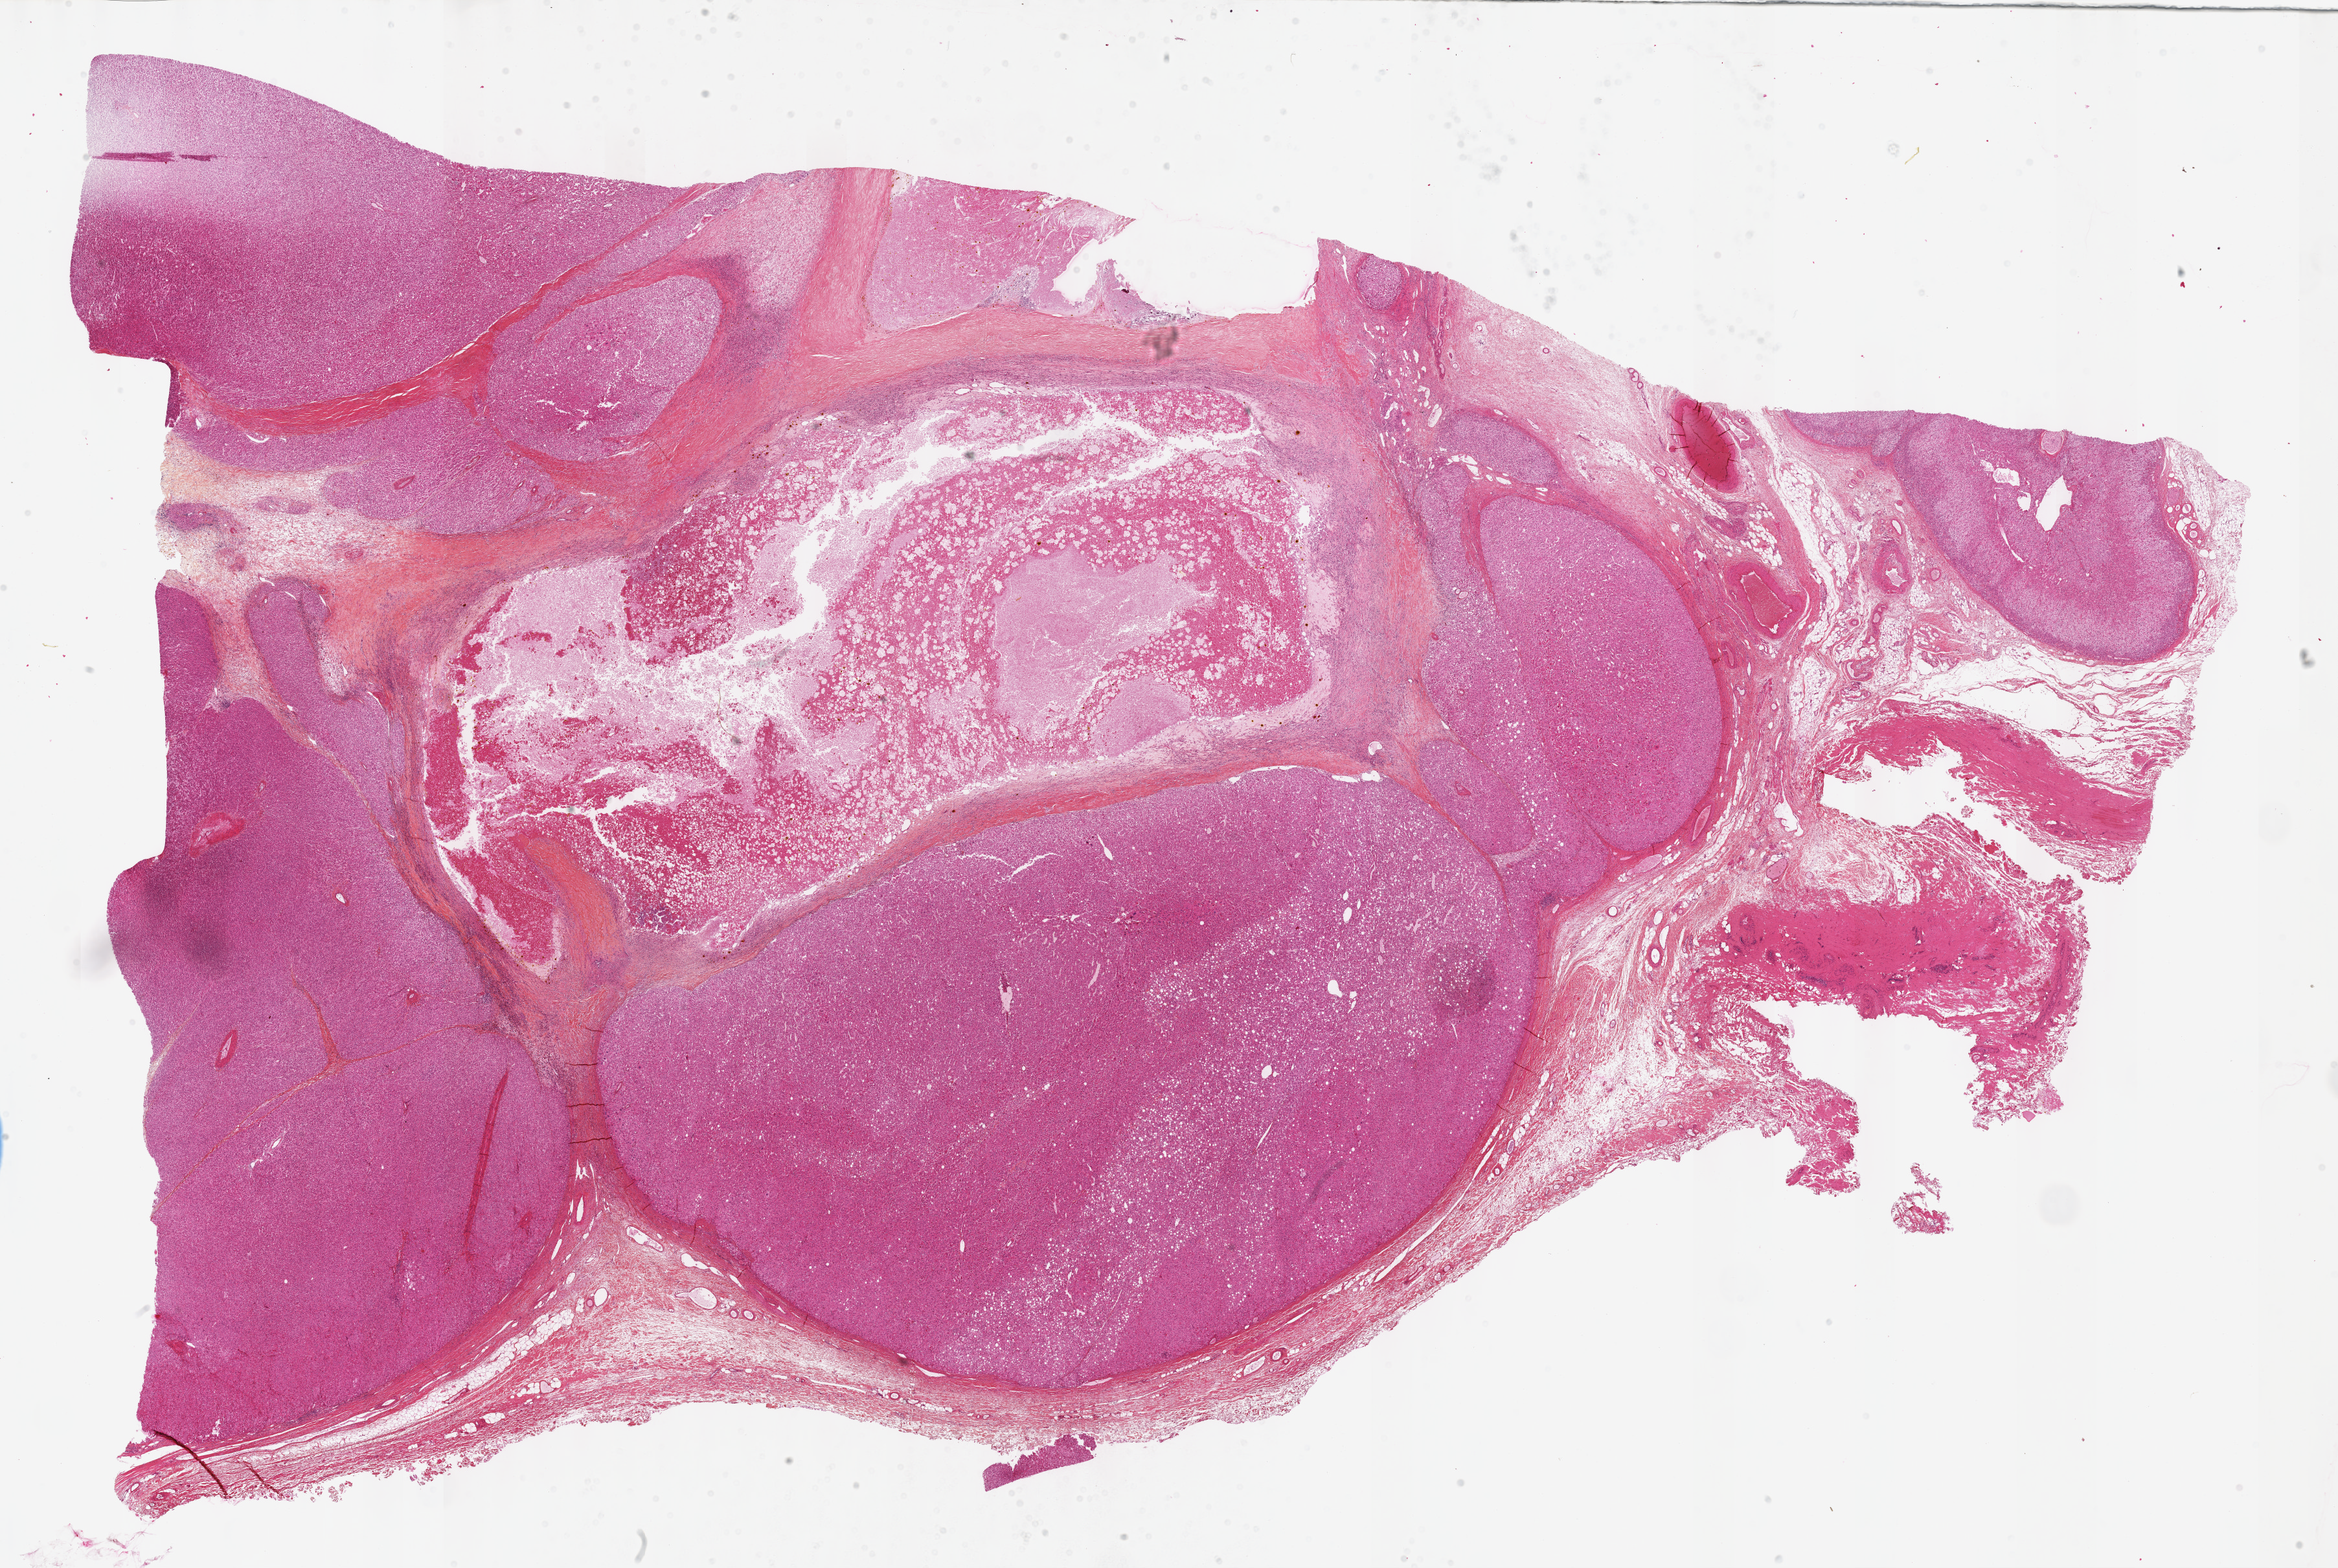
H&E-stained whole-slide image, a low-resolution overview of the entire scanned area, about 29.2 x 19.6 mm (acquisition: 40x scan). FFPE section. Primary tumour sample from the adrenal cortex. Female patient; age at initial diagnosis 30 years.
Diagnosis: Adrenal cortical carcinoma (cortex of adrenal gland).